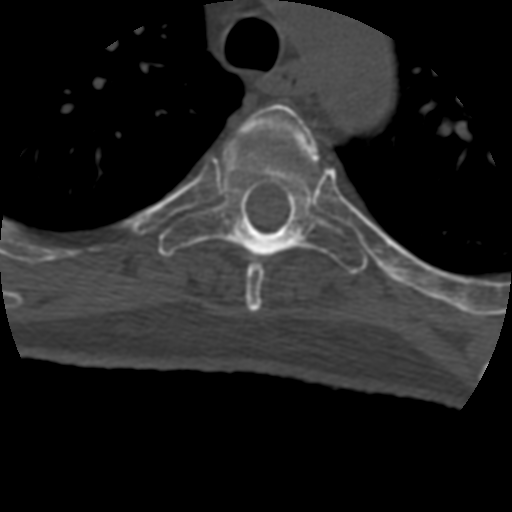
CT including the spine, one axial slice; 120 kVp; bone window (W 1800 / L 400 HU); 1.25 mm slice thickness; 512 × 512 image matrix. Patient age 69 years. From the clinical record (not read from this slice): primary cancer: prostate.
Structures marked on this image (semi-automatically segmented with operator editing):
- T4 vertebra: box from (x=241, y=103) to (x=319, y=312) px
- T5 vertebra: (x=158, y=138)–(x=368, y=274)